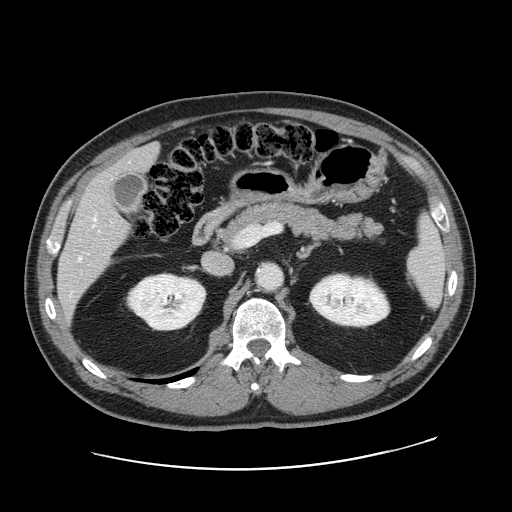
Contrast-enhanced abdominal CT, one axial slice; position 87 of 178 along the scan axis; 120 kVp; intravenous contrast given; soft-tissue window (W 400 / L 40 HU); 2.5 mm slice thickness; 512 × 512 image matrix. Male patient, age 63 years. Case-level facts recorded for this patient, not image findings: diagnosis: colorectal cancer liver metastases, imaged before liver resection; multiple liver metastases: yes; largest metastasis: 8 cm; chemotherapy before resection: no.
Structures marked on this image (outlined manually by an expert reader):
- hepatic veins: bounding box (x1, y1, x2, y2) in pixels: (78, 217, 96, 260)
- liver: (58, 146, 157, 312)
- planned liver remnant (the part of the liver to remain after resection): (113, 146, 157, 172)